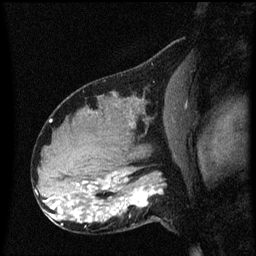
Breast MRI (dynamic contrast-enhanced), one sagittal slice. Slice 33 of 60 in the series (ordered by position). Dynamic contrast-enhanced series, image 2 of 3 at this slice position (ordered by acquisition). 1.5 T. TE 4.2 ms, TR 8.4 ms. 256 × 256 image matrix. Female patient, age 31 years. Case-level facts recorded for this patient, not image findings: setting: breast cancer imaged before/during neoadjuvant chemotherapy; receptor status: HR-positive, HER2-negative.
Outlined on this slice (semi-automatic segmentation, software-assisted and operator-edited):
- analysis volume of interest (the breast-tissue region the enhancement analysis was run in; not a lesion): bounding box [x1, y1, x2, y2] px = [102, 166, 169, 229]
- tumour enhancement mask (voxels above the 70 % enhancement threshold inside the analysis volume of interest): [114, 178, 163, 215]